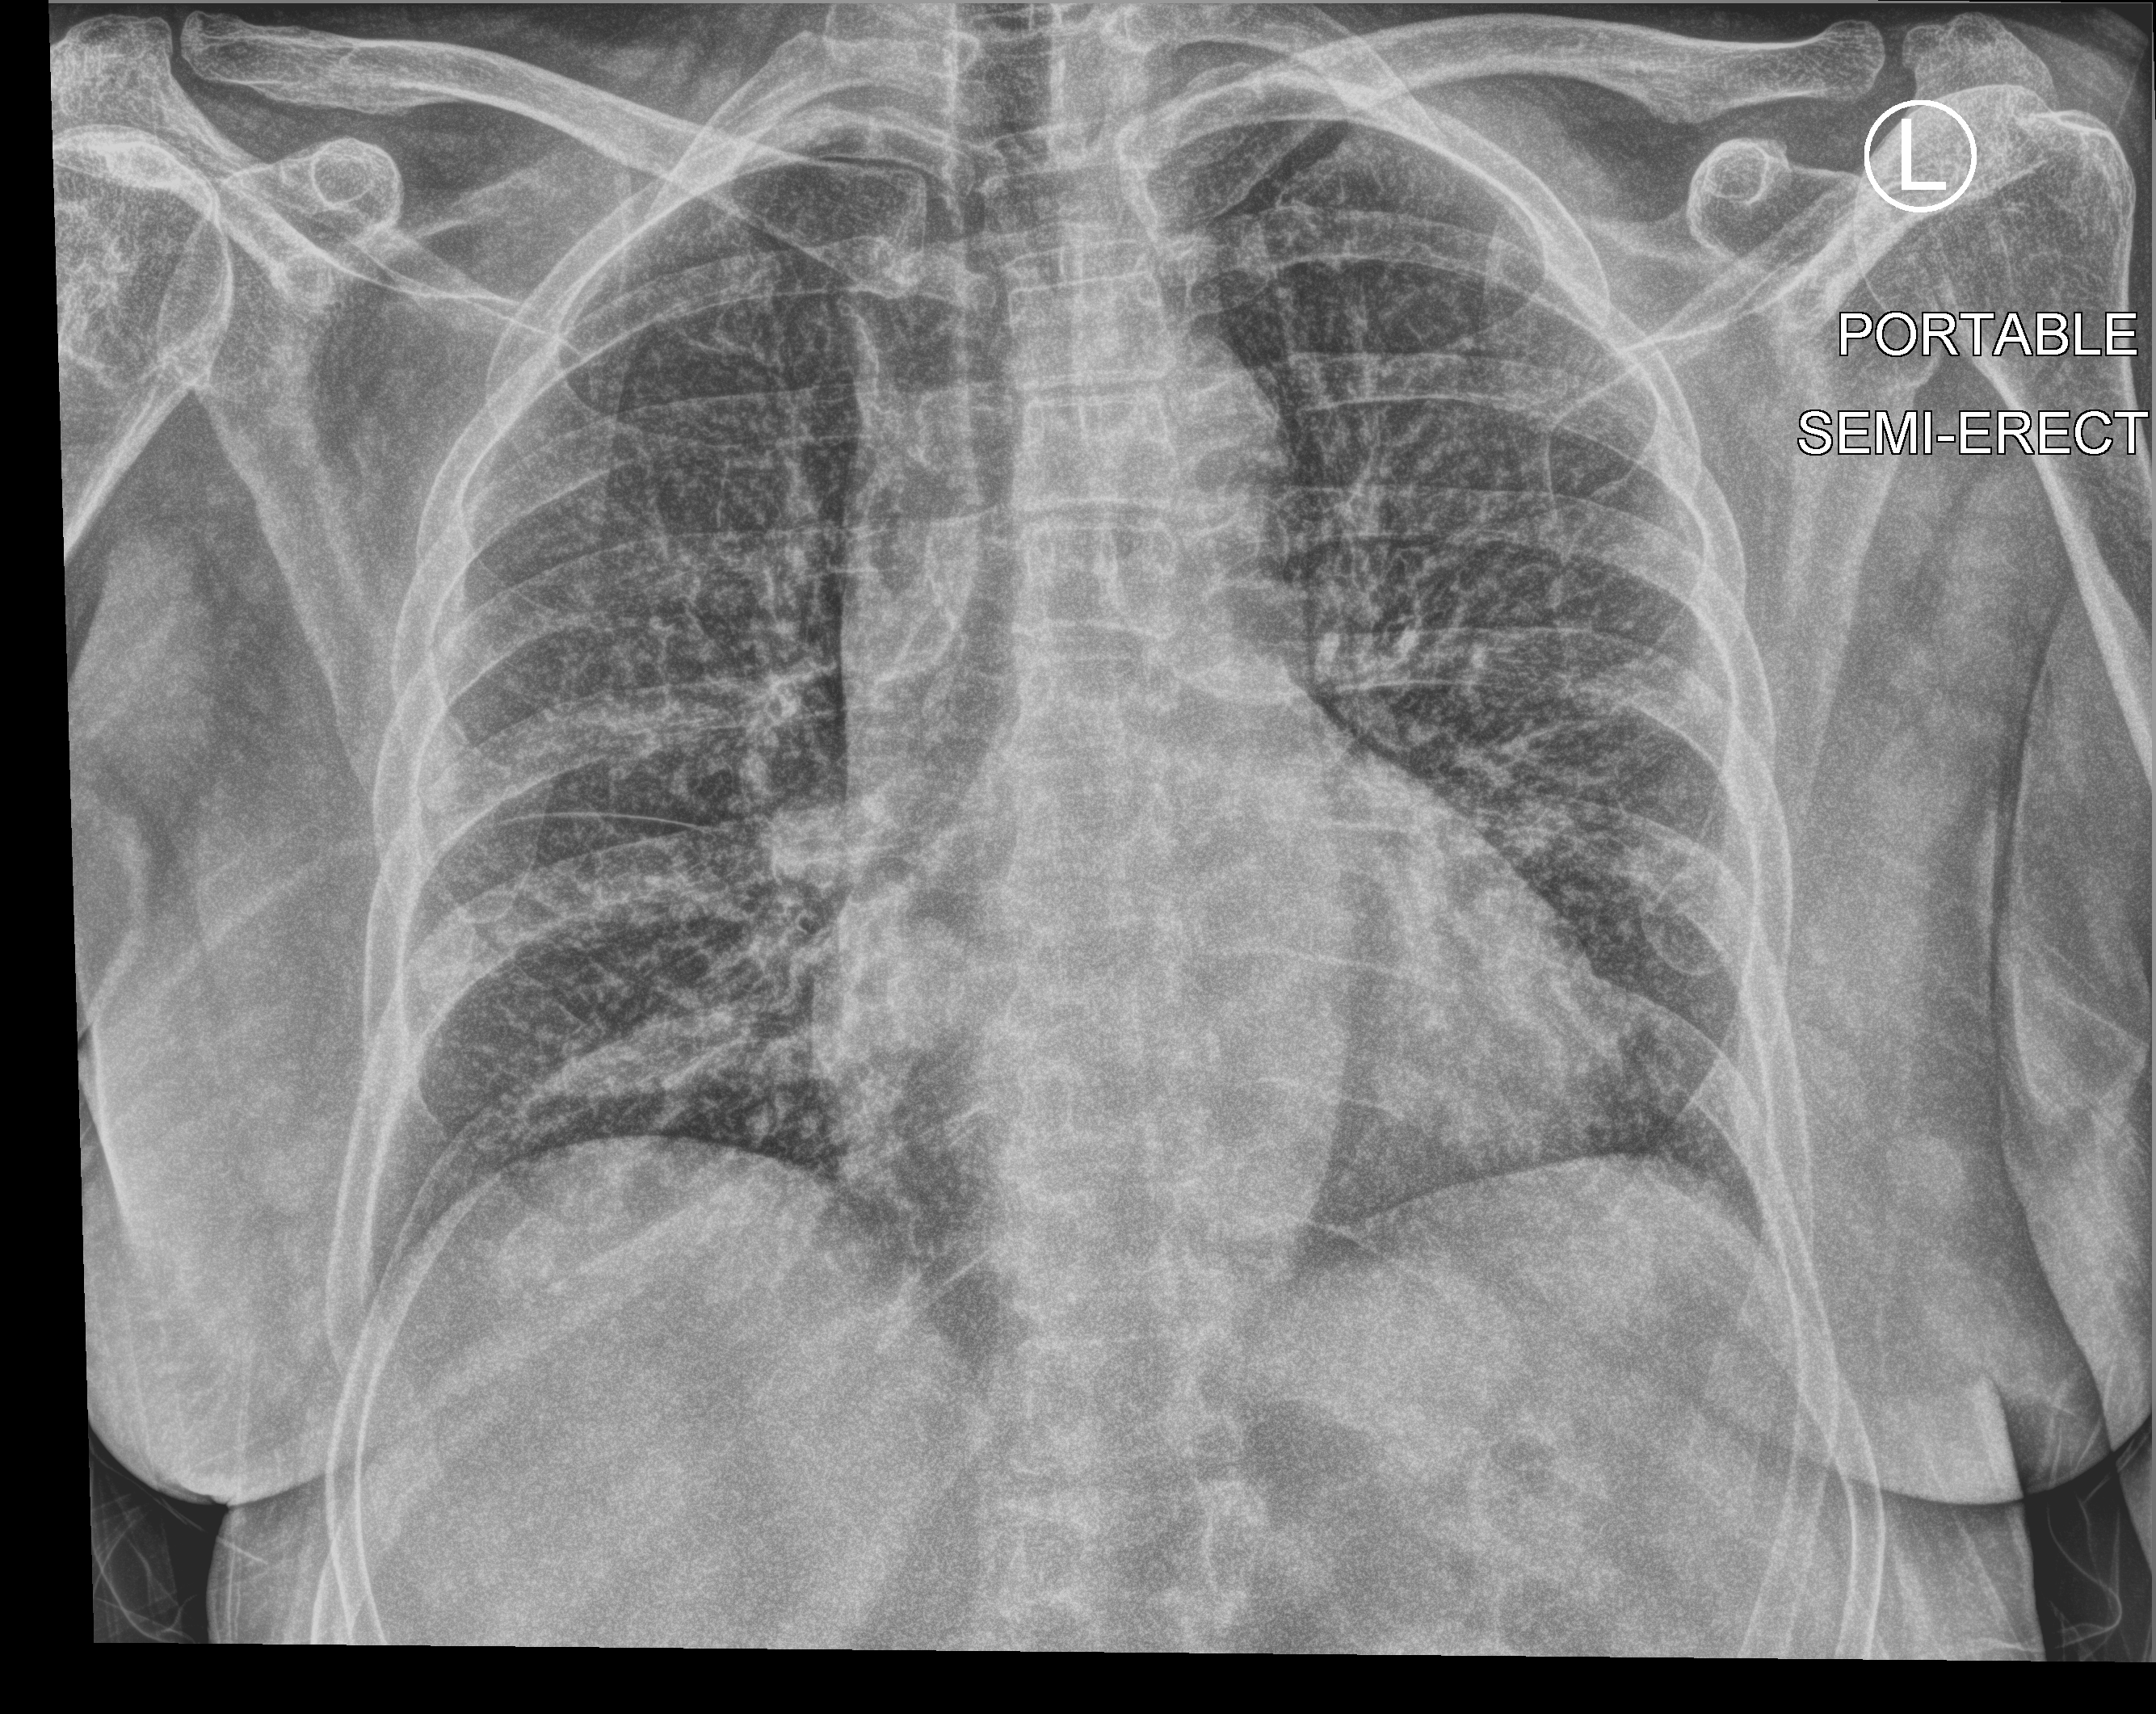
Chest X-ray (portable), anteroposterior (AP) projection. Patient hospitalised with COVID-19; female, aged 60–74 years.
Admission-level facts for this patient (not findings on this image; timing relative to this image not recorded): mechanically ventilated during this hospital stay: no; admitted to intensive care during this hospital stay: no.